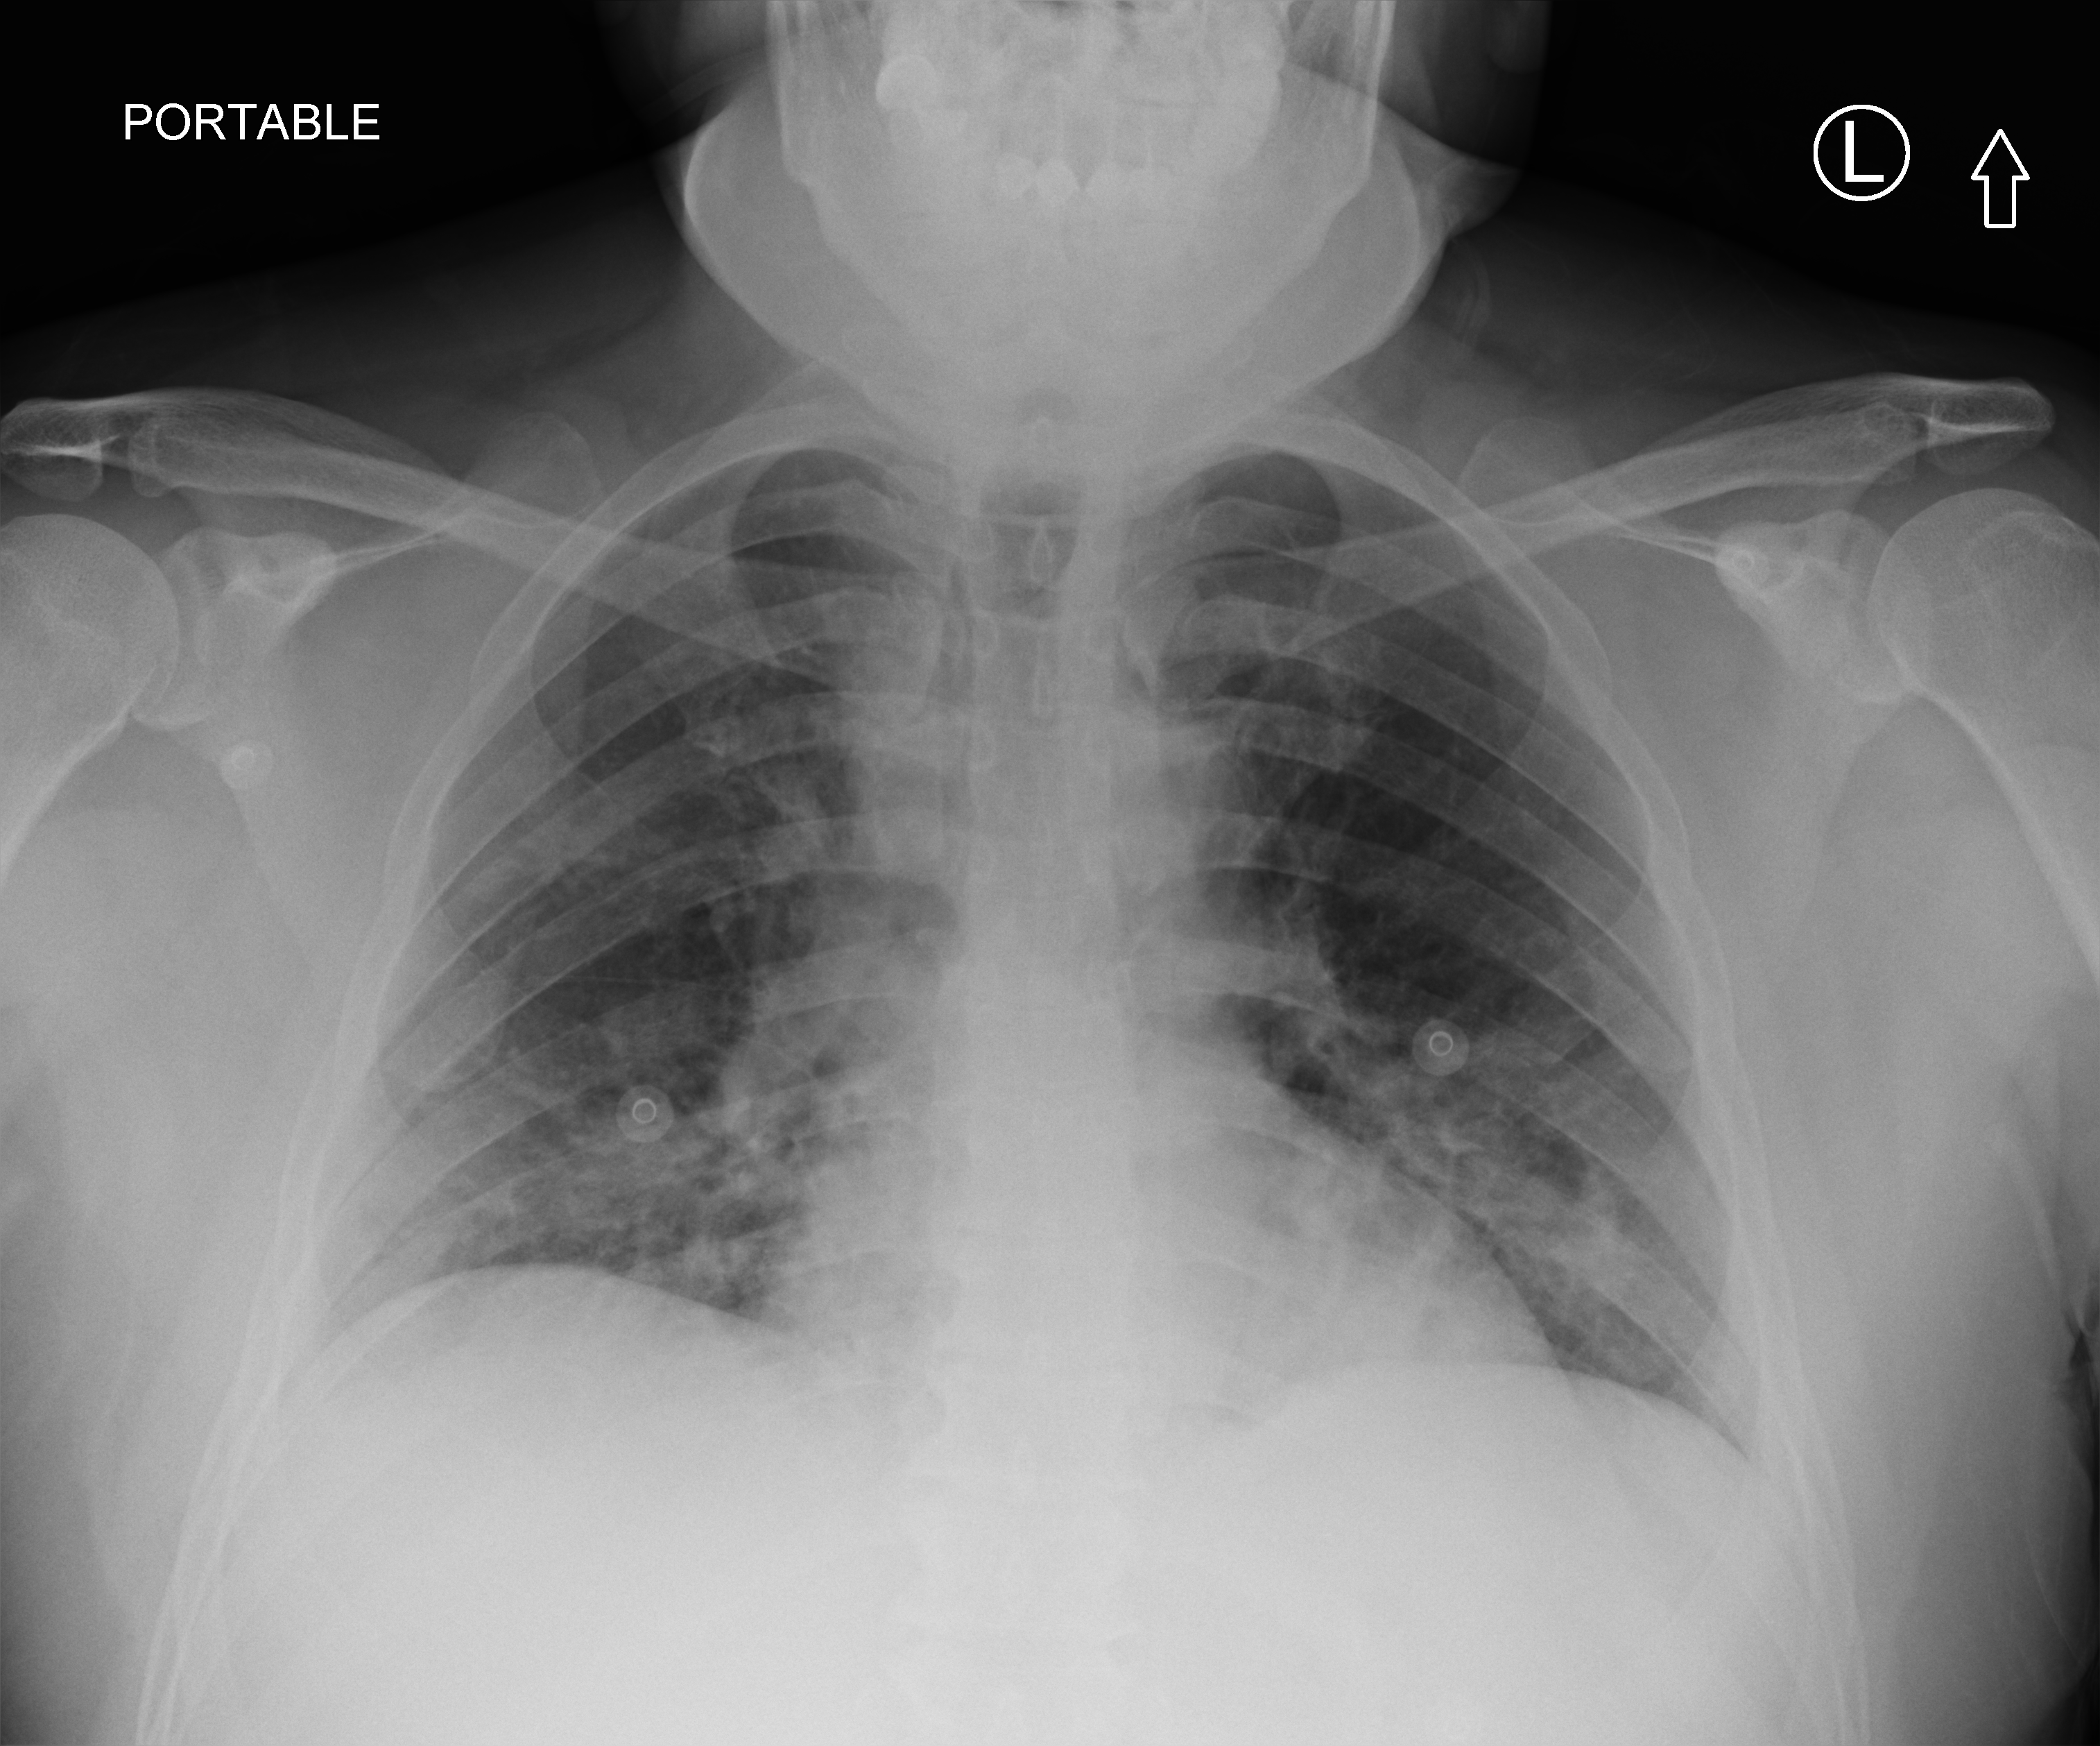
Portable chest radiograph, anteroposterior (AP) projection. Patient hospitalised with COVID-19; male, aged 18–59 years.
Hospital-stay facts (about this admission, not read from this image; timing relative to this image not recorded): admitted to intensive care during this hospital stay: no; mechanically ventilated during this hospital stay: no; hypertension (admission record): yes.